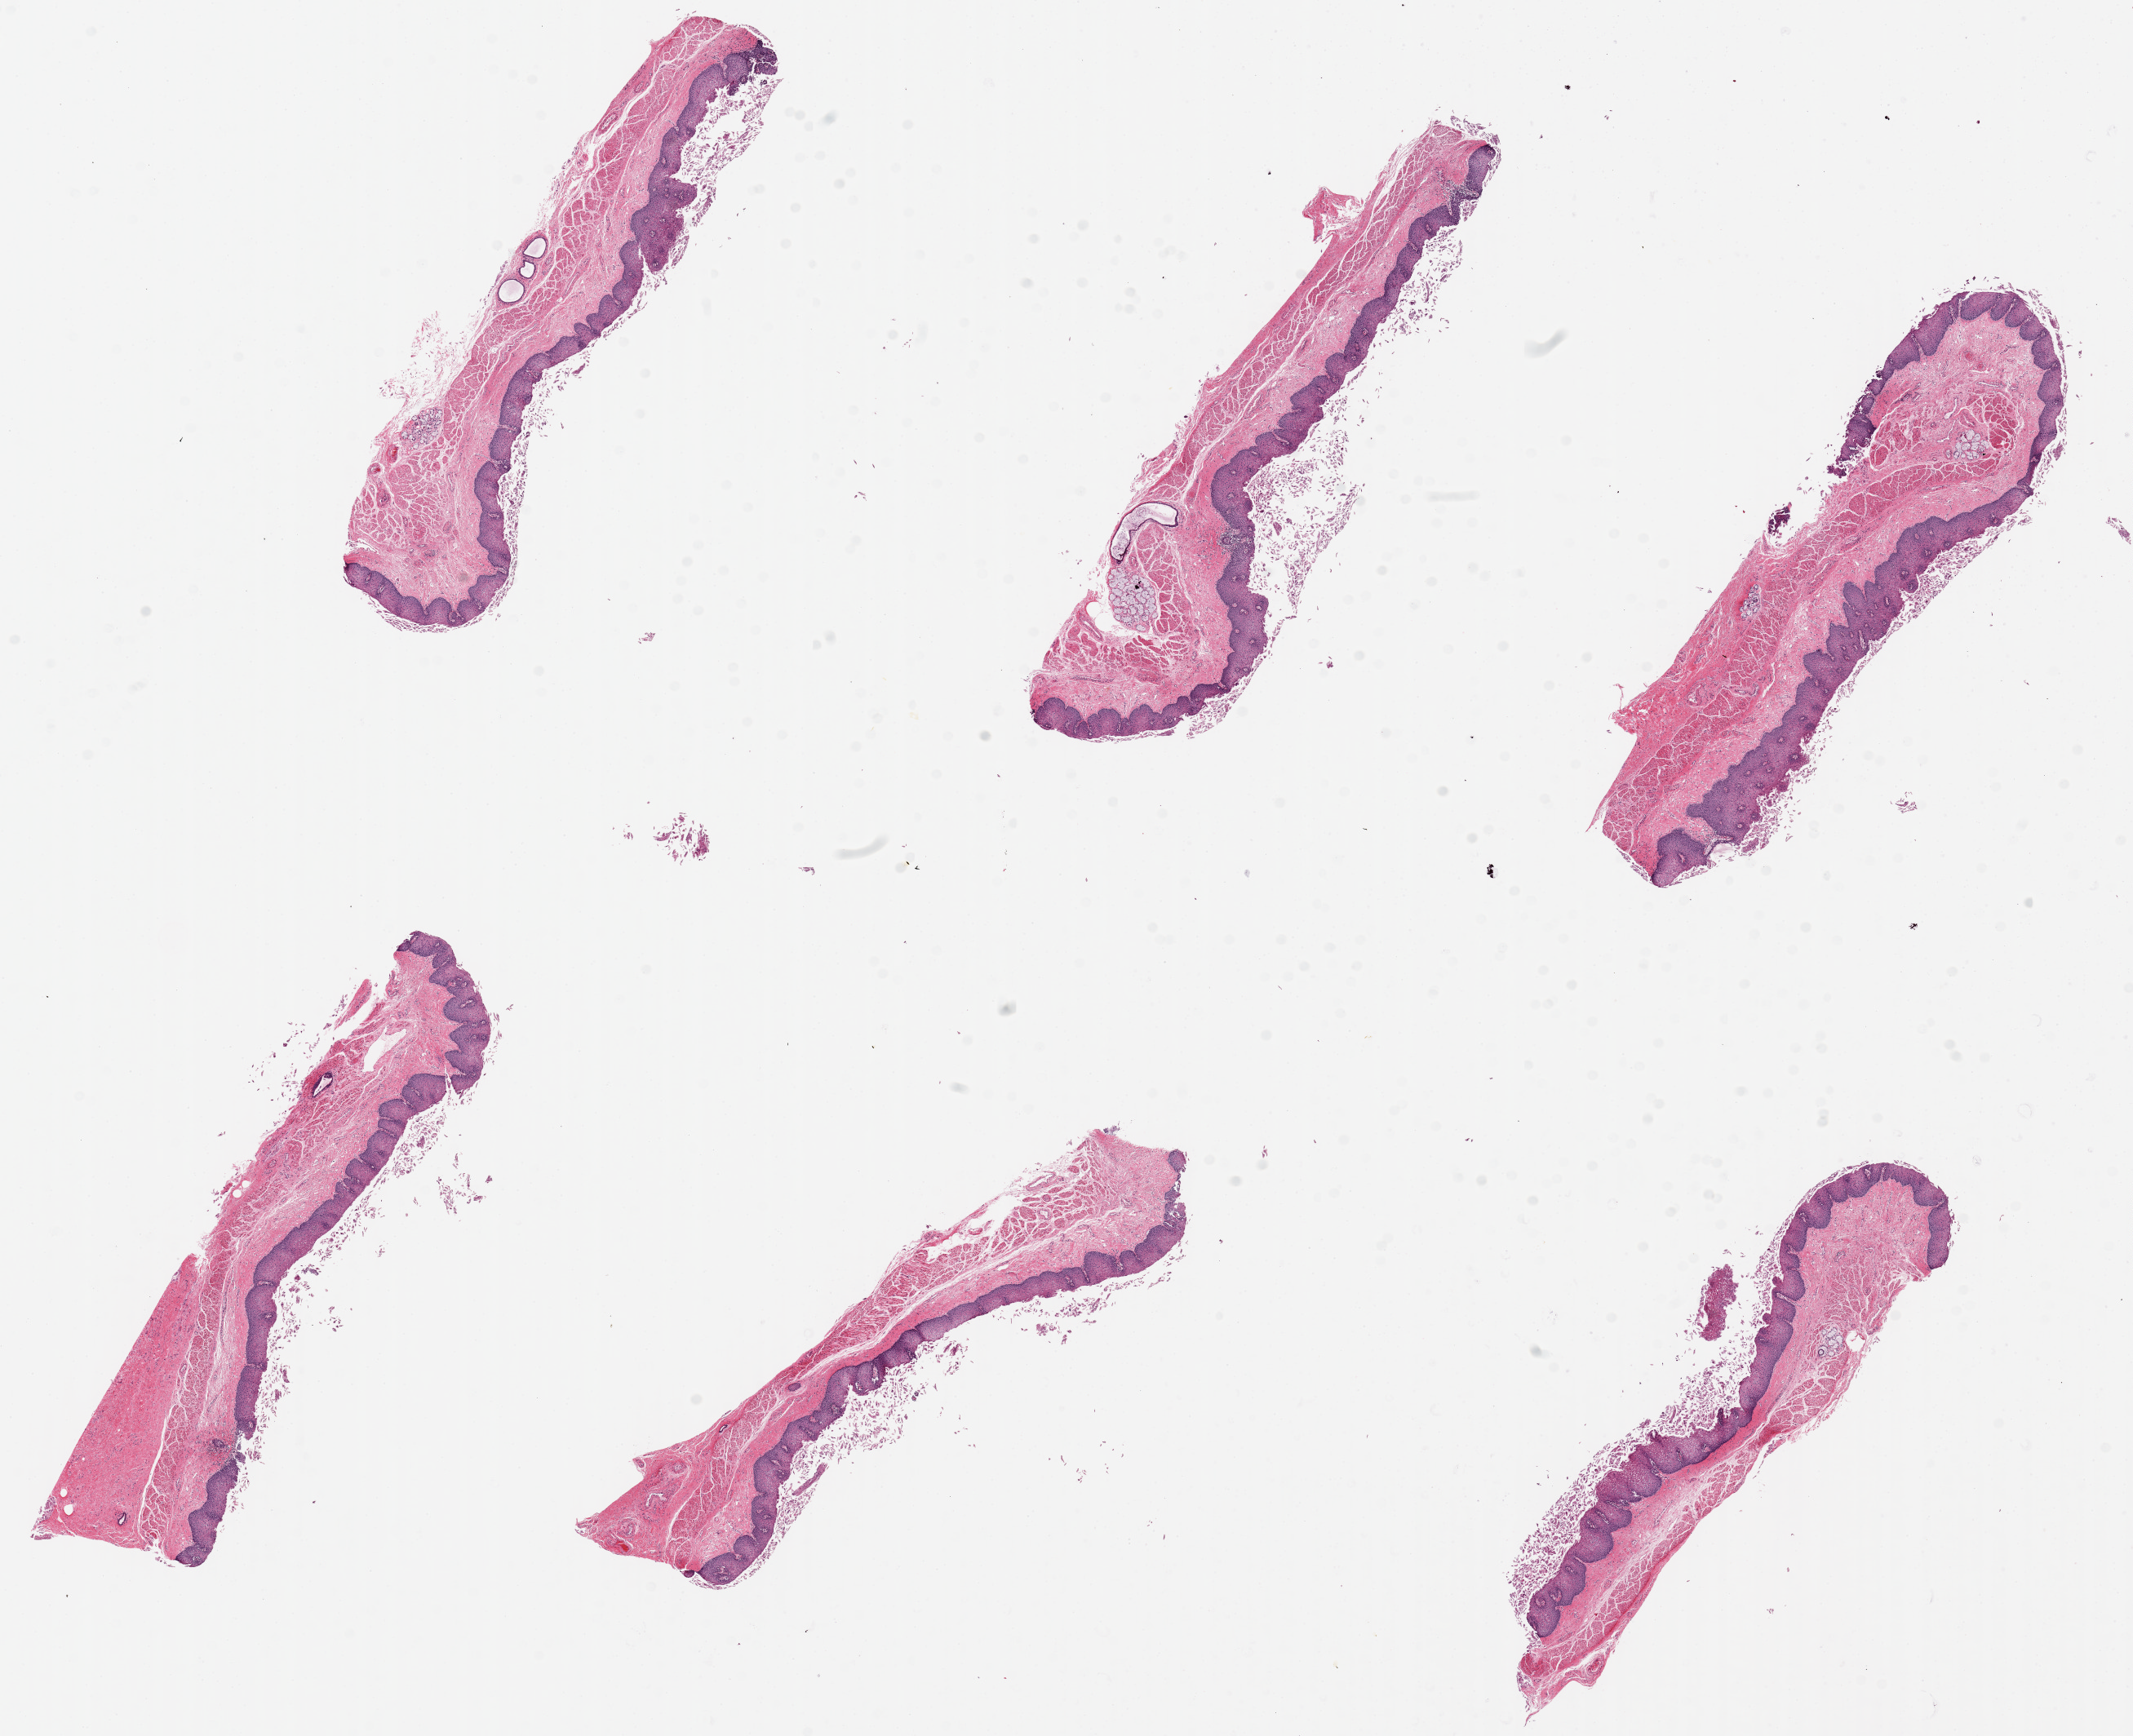
Whole-slide image, hematoxylin and eosin (H&E) stain, brightfield — shown as a low-resolution overview of the whole scanned area (about 20.7 x 16.8 mm), PAXgene-fixed, paraffin-embedded tissue, sampled site (target tissue): esophageal mucous membrane, tissue donor sample. Female donor.
* review note (as recorded): 6 pieces. up to 7x2mm; well dissected mucosa